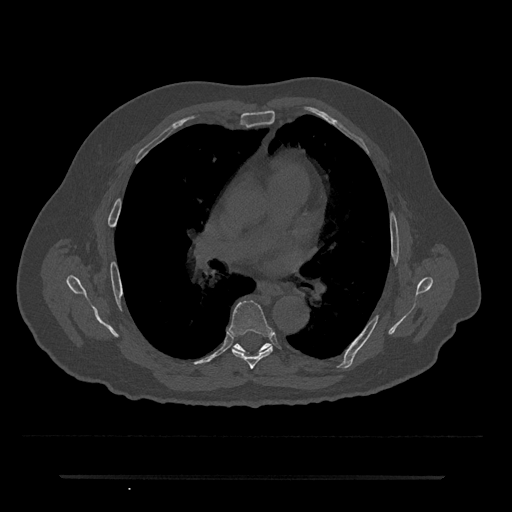
CT including the spine, one axial slice. Slice 422 of 797 in the series (ordered by position). 120 kVp. Bone window (W 1800 / L 400 HU). 0.5 mm slice thickness. 512 × 512 image matrix. Patient: male, 69 years. From the clinical record (not read from this slice): primary cancer: prostate.
Outlined on this slice (semi-automatic segmentation, software-assisted and operator-edited):
- T6 vertebra: bounding box (x1, y1, x2, y2) in pixels: (229, 300, 274, 369)
- T7 vertebra: (233, 344, 270, 351)